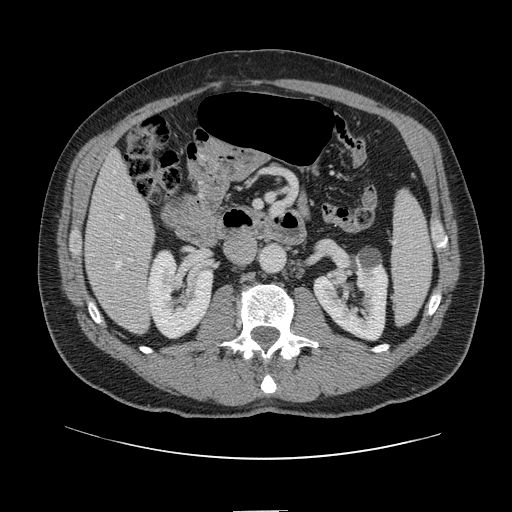
Contrast-enhanced abdominal CT, one axial slice. Slice 40 of 161 in the series (ordered by position). 120 kVp. Intravenous contrast given. Soft-tissue window (W 400 / L 40 HU). 512 × 512 image matrix, field of view 412 × 412 mm. Male patient, age 66 years. From the clinical record (not read from this slice): diagnosis: colorectal cancer liver metastases, imaged before liver resection; multiple liver metastases: no; largest metastasis: 3.5 cm; disease in both lobes: no.
Outlined on this slice (expert manual segmentation):
- hepatic veins: box from (x=117, y=215) to (x=124, y=267) px
- liver: (x=86, y=154)–(x=154, y=334)
- planned liver remnant (the part of the liver to remain after resection): (x=86, y=154)–(x=151, y=269)